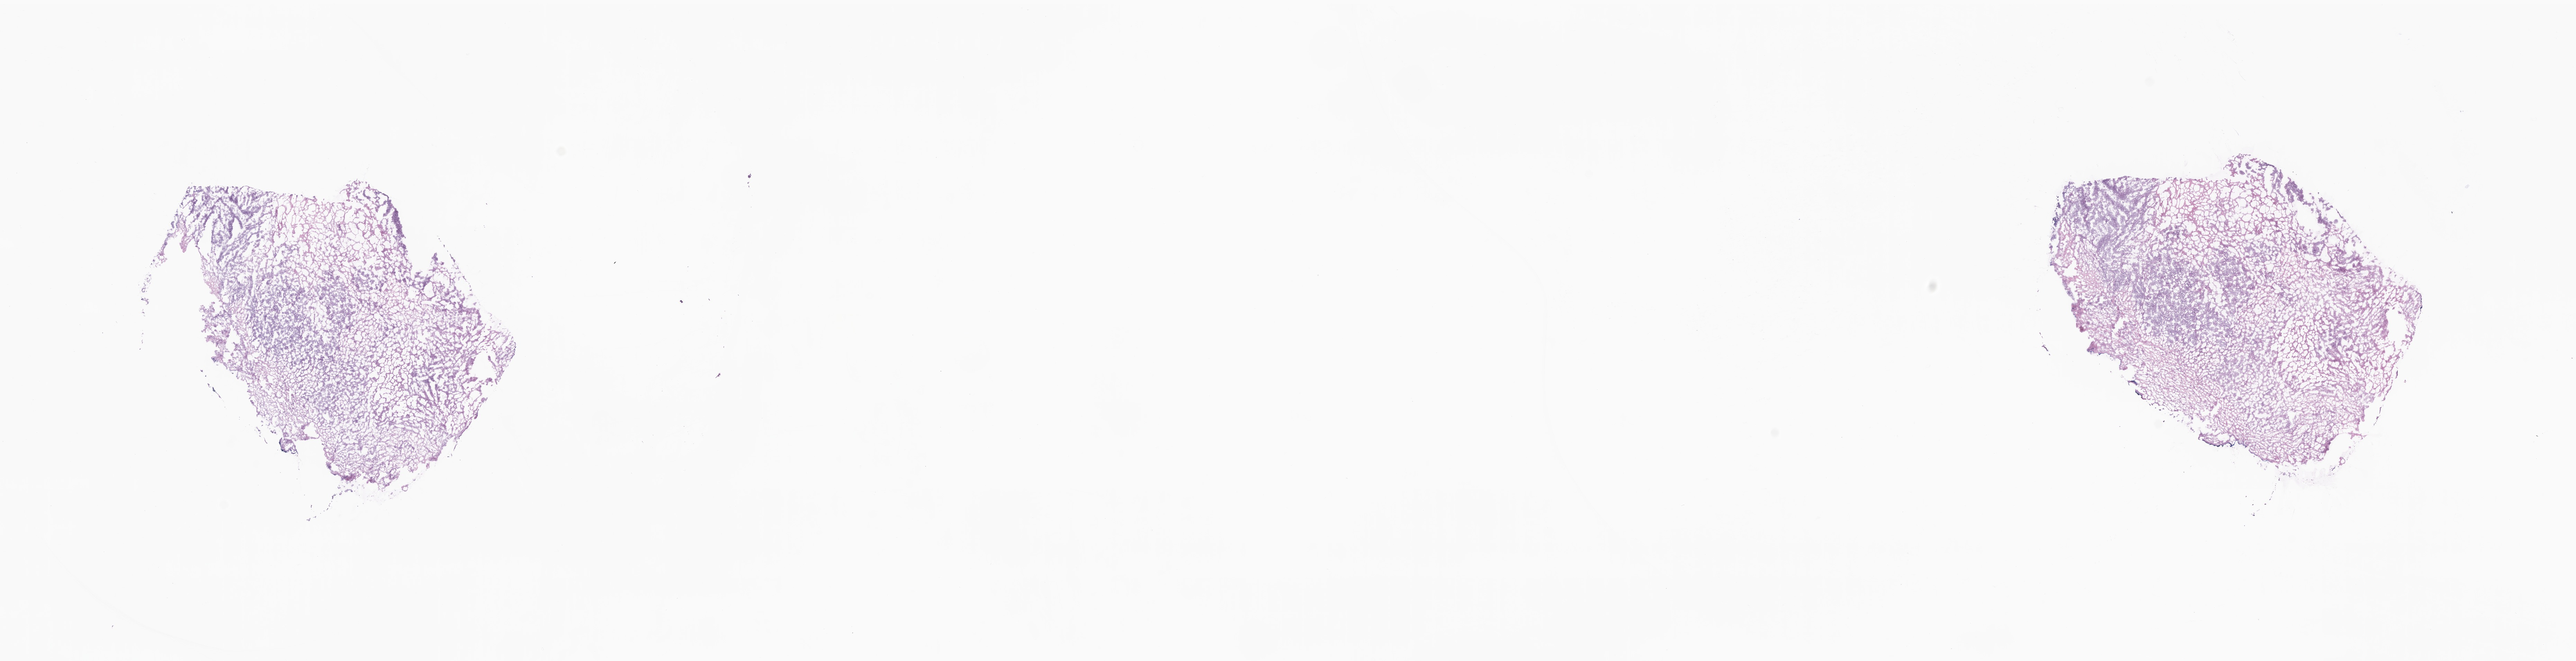
Whole-slide image, haematoxylin and eosin stain, whole scanned area (about 31.4 x 8.0 mm) shown as a low-resolution overview. Cryosection. Metastatic tumor tissue. Female patient. Composition of this section per pathologist review: tumor cells 65%, tumor nuclei 74%, stromal cells 0%, necrosis 5%, normal cells 30%. Inflammatory infiltration, as recorded: lymphocyte infiltration 0%, monocyte infiltration 0%, neutrophil infiltration 0%.
- section: bottom of the tissue portion
- patient diagnosis (primary): Serous surface papillary carcinoma